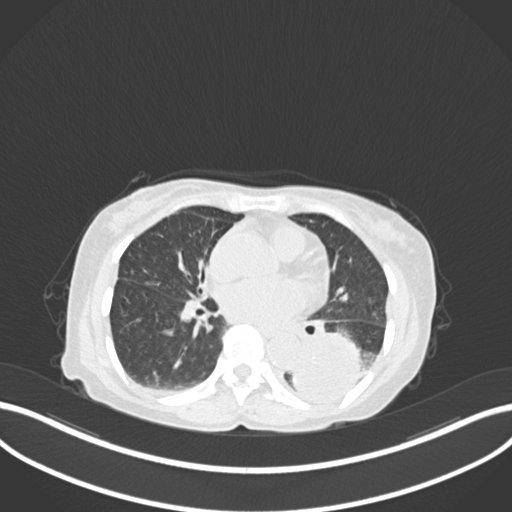
Chest CT, one axial slice. Slice 67 of 233 in the series (ordered by position). Reconstruction kernel B30f. Lung window (W 1500 / L -600 HU). 1 mm slice thickness. 512 × 512 image matrix, field of view 400 × 400 mm. Female patient, age 78 years. Case-level facts recorded for this patient, not image findings: clinical TNM (as recorded): T3 N0 M1.
Outlined on this slice (rectangle marked by the reading radiologist):
- lung tumour (recorded histology: squamous cell carcinoma): bounding box [x1, y1, x2, y2] px = [288, 329, 367, 407]